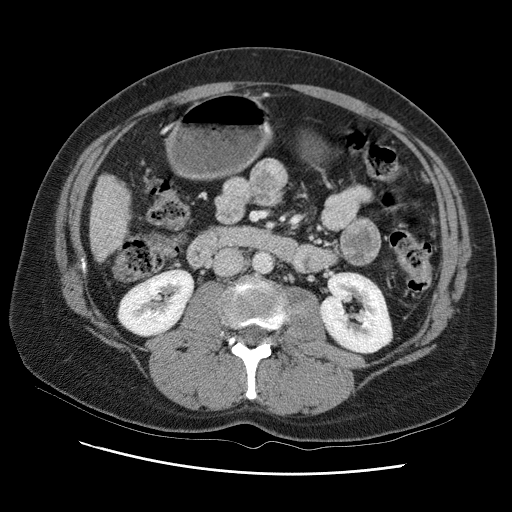
Contrast-enhanced abdominal CT (liver protocol), one axial slice; slice 23 of 95 in the series (ordered by position); 120 kVp; one of 2 acquisitions stored at this slice position; soft-tissue window (W 400 / L 40 HU); 2.5 mm slice thickness; 512 × 512 image matrix. From the clinical record (not read from this slice): diagnosis: hepatocellular carcinoma (patient treated with transarterial chemoembolisation; whether this scan precedes or follows treatment is not stated here); TNM stage (as recorded): Stage-I; Child-Pugh class: B; tumour nodularity: uninodular.
Outlined on this slice (semi-automatic segmentation, software-assisted and operator-edited):
- liver parenchyma outside the tumour (the mass and vessels are separate outlines, so this box may not span the whole liver): bounding box (x1, y1, x2, y2) in pixels: (90, 158, 144, 262)
- liver vessels: (102, 195, 121, 244)